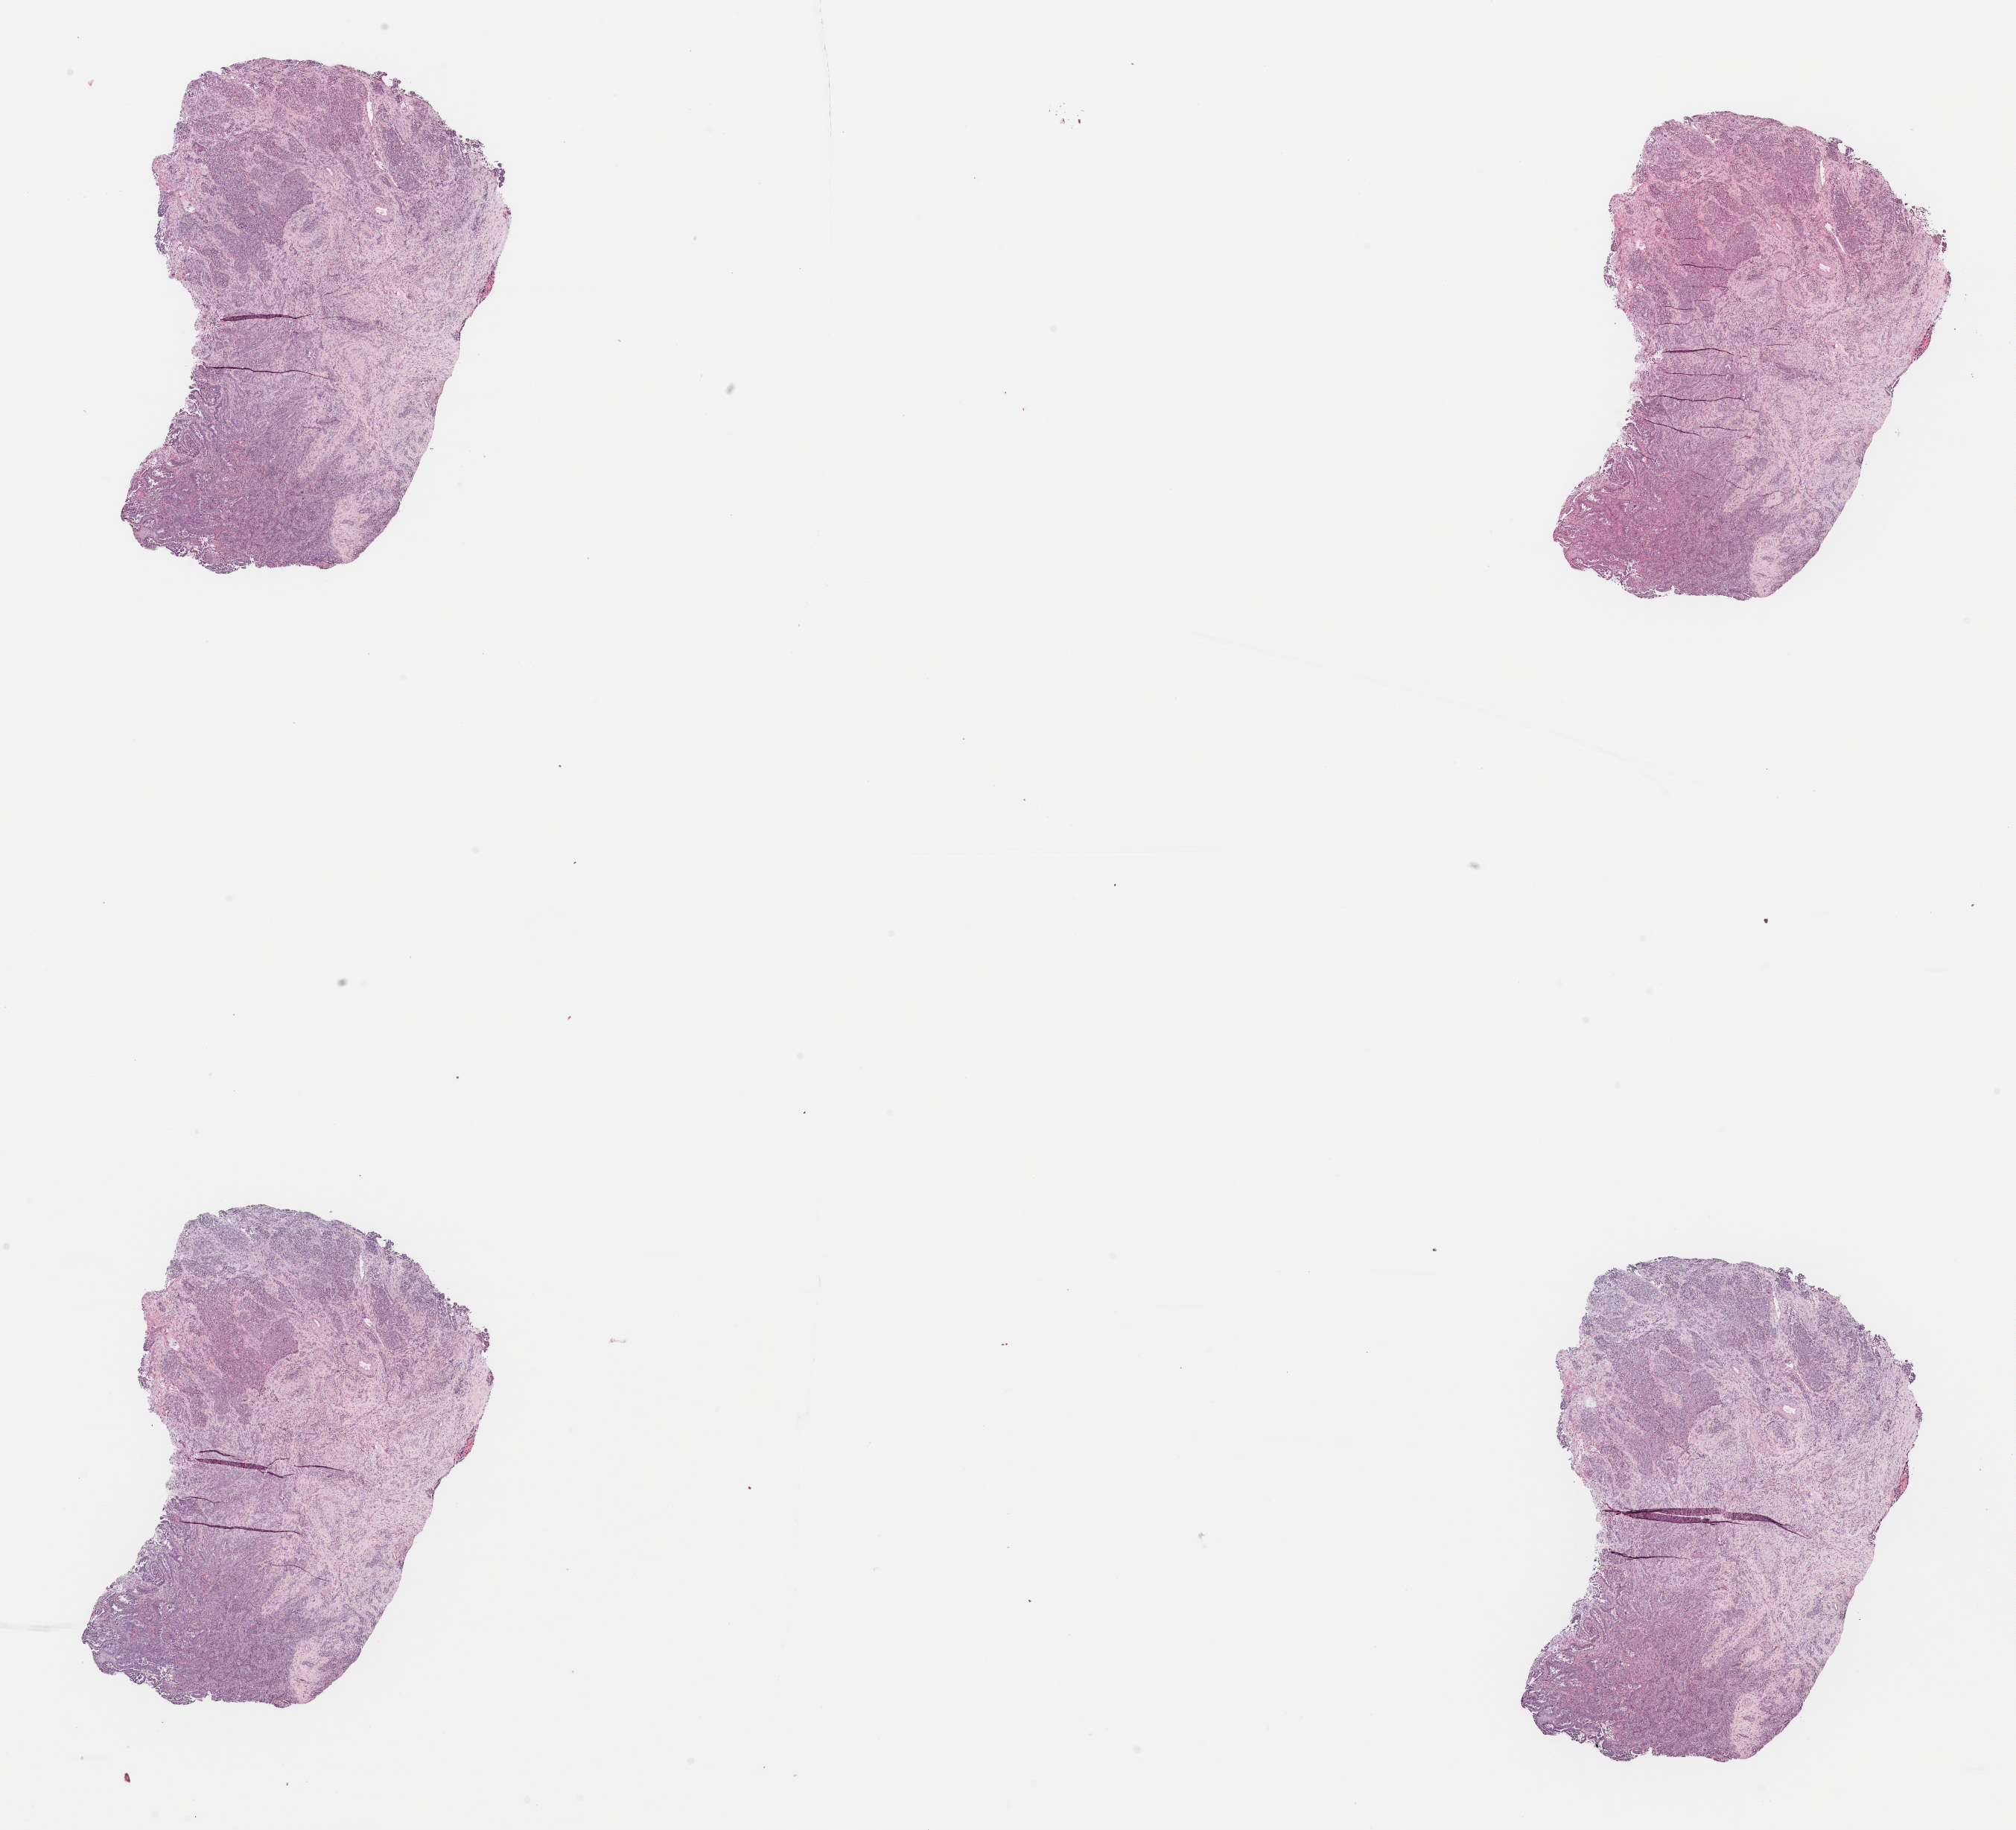
Hematoxylin and eosin (H&E) stained whole-slide image — whole scanned area (about 21.4 x 19.4 mm, from a 40x scan) shown as a low-resolution overview. Formalin-fixed paraffin-embedded (FFPE) diagnostic section. Uterus, primary tumour sample. Female, age 69 years at initial diagnosis. Histologic grade: G3 (poorly differentiated).
• pathologic diagnosis: Serous cystadenocarcinoma, NOS (endometrium)
• FIGO stage: IIIC